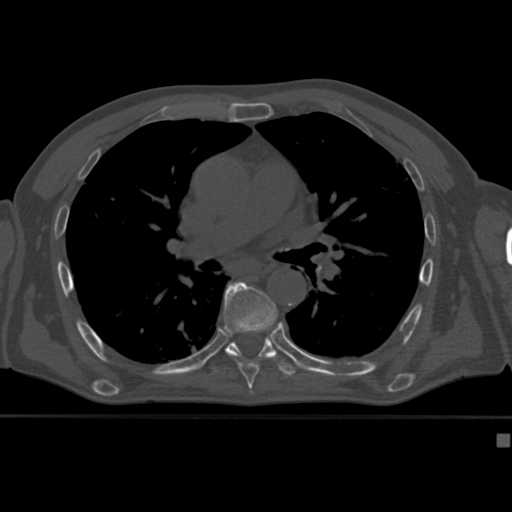
CT including the spine, one axial slice; slice 273 of 430 in the series (ordered by position); reconstruction kernel Br40s; bone window (W 1800 / L 400 HU); 1.5 mm slice thickness; 512 × 512 image matrix, field of view 337 × 337 mm. Male patient, age 64 years. From the clinical record (not read from this slice): primary cancer: uterus; vertebrae with lytic lesions (as recorded): T1, T4, T5, T7, L5.
Annotated regions visible in this slice (semi-automatic segmentation, software-assisted and operator-edited):
- T7 vertebra: bounding box [x1, y1, x2, y2] px = [223, 281, 277, 382]
- T8 vertebra: [213, 282, 297, 377]